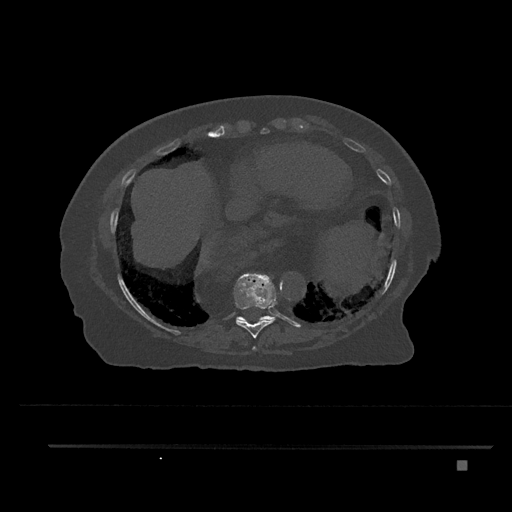
CT including the spine, one axial slice. Position 388 of 797 along the scan axis. 120 kVp. Bone window (W 1800 / L 400 HU). 0.5 mm slice thickness. 512 × 512 image matrix. Patient: female, 76 years. Case-level facts recorded for this patient, not image findings: primary cancer: lung; vertebrae with lytic lesions (as recorded): T11, L3.
Structures marked on this image (semi-automatic segmentation, software-assisted and operator-edited):
- T10 vertebra: bounding box <236,315,275,323> (left, top, right, bottom; pixels)
- T8 vertebra: <252,346,257,351>
- T9 vertebra: <234,273,277,338>